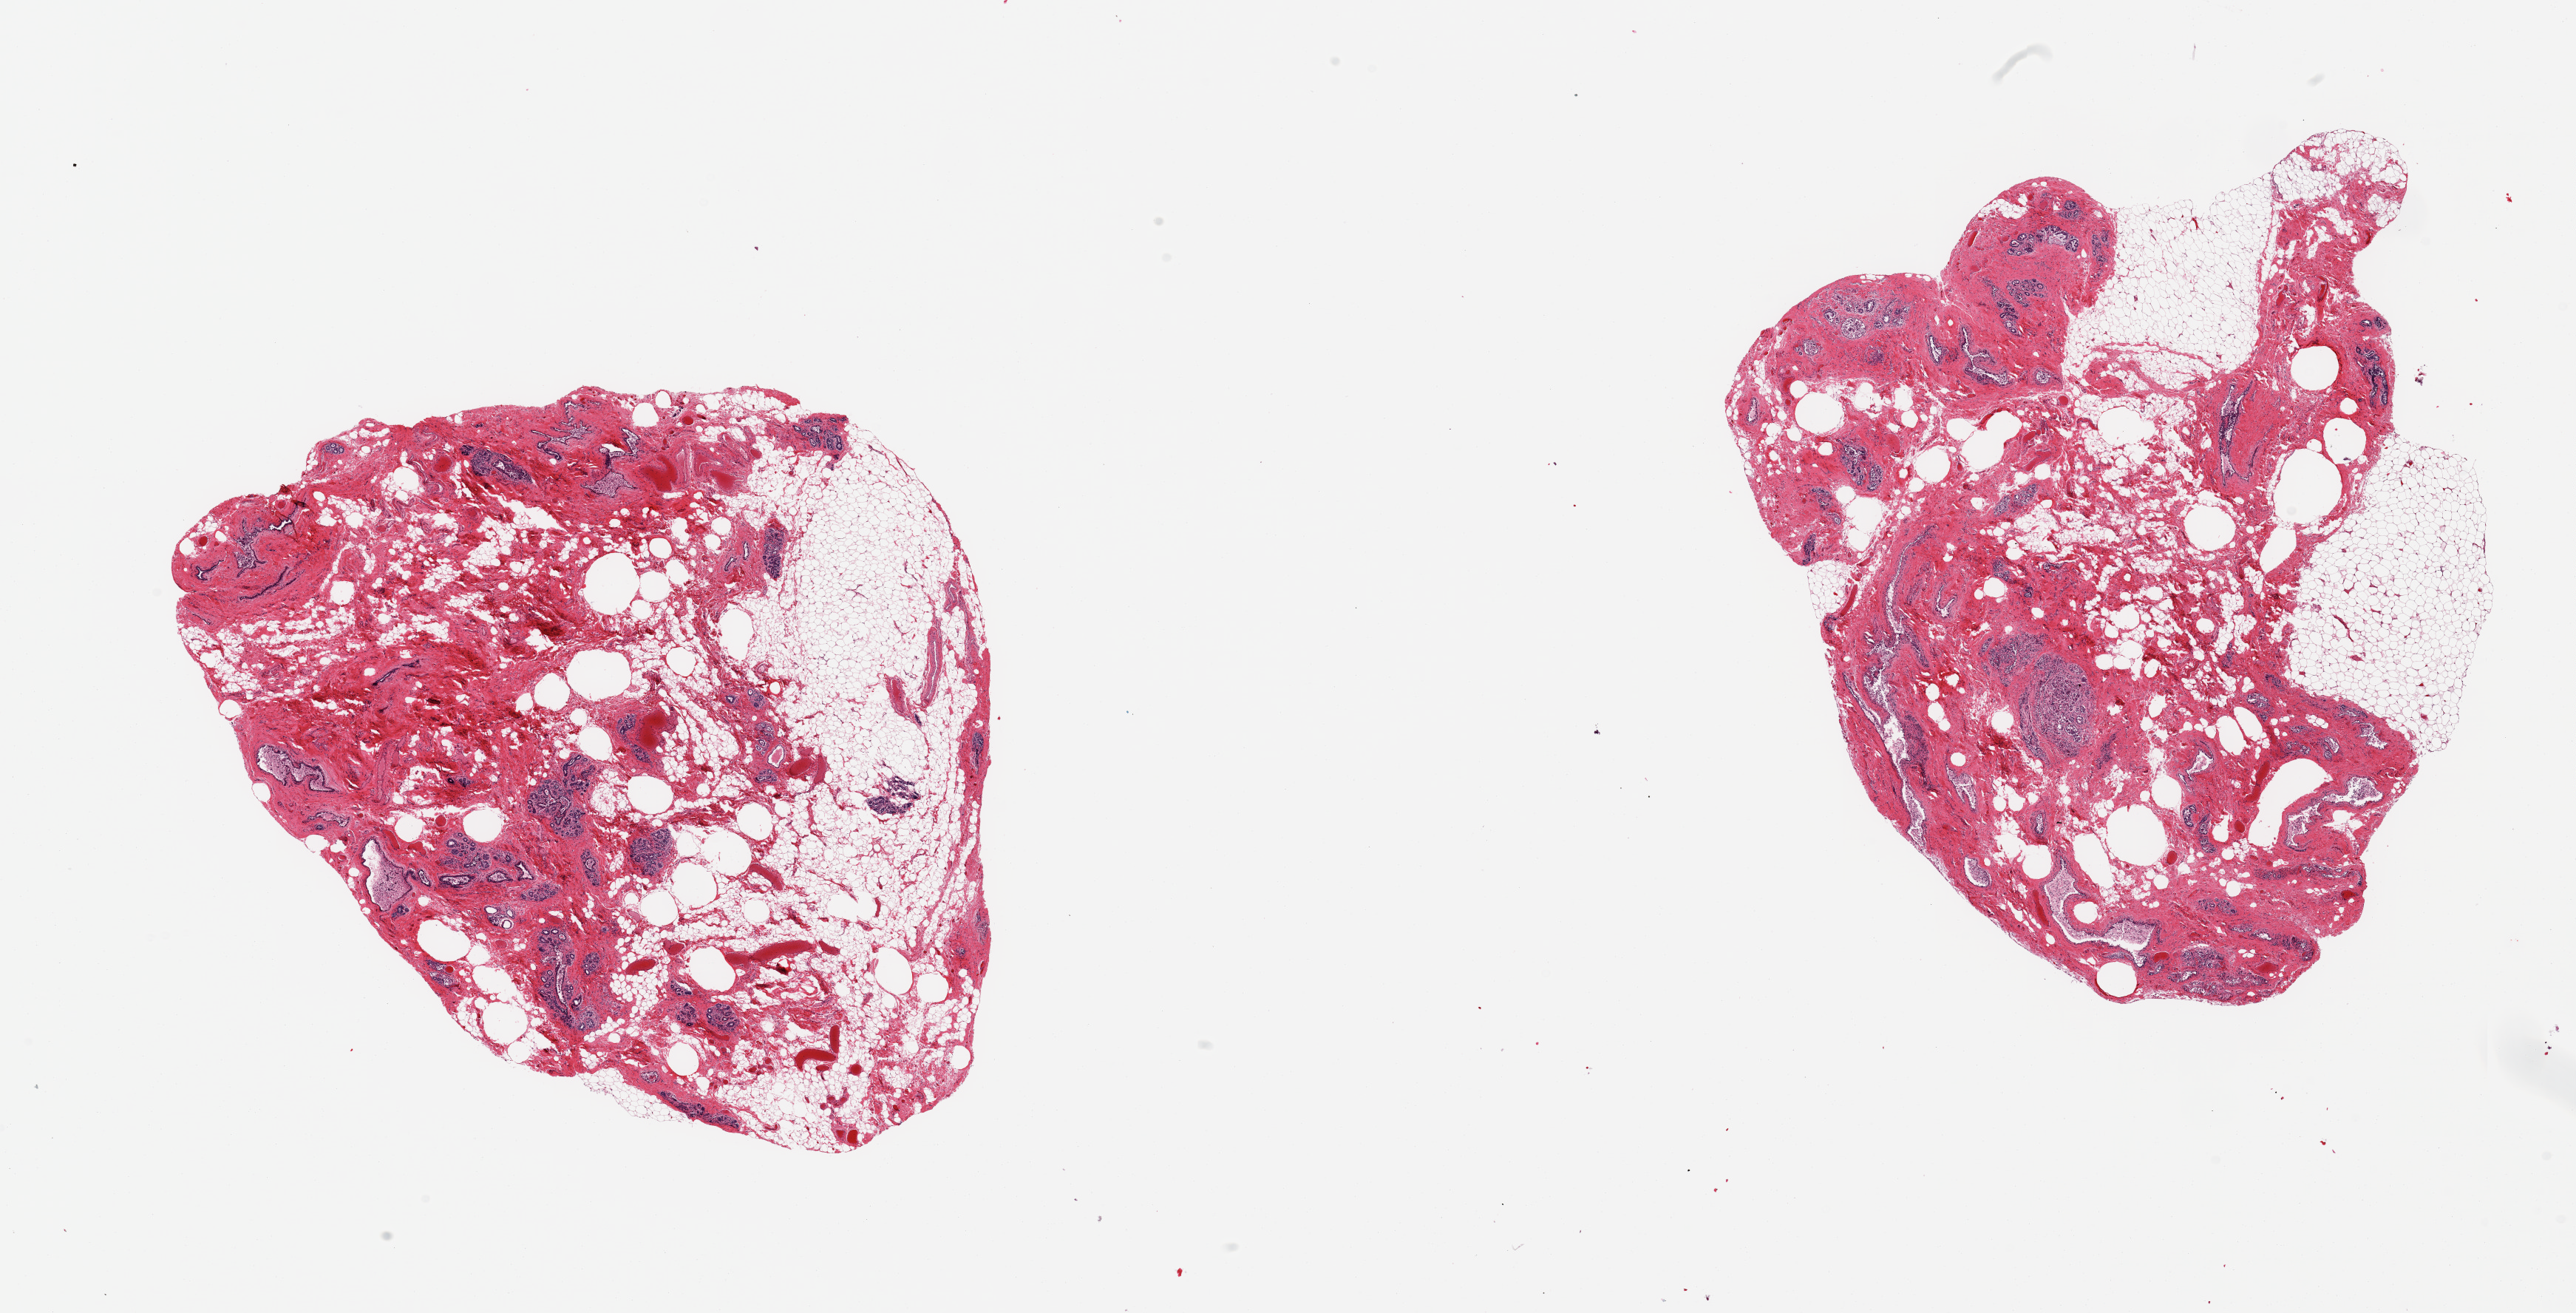
Whole-slide image, H&E stain, a low-resolution overview of the entire scanned area, about 27.6 x 14.0 mm; PAXgene-fixed paraffin-embedded (PFPE) section; section of breast (target tissue); donor tissue sample. Donor sex: female.
Pathologist's review note for this sample: 2 pieces; fat and abundant dense fibrocollagenous stroma with multiple ducts and lobules with sloughing lining. Focal proliferation and microcalcification.